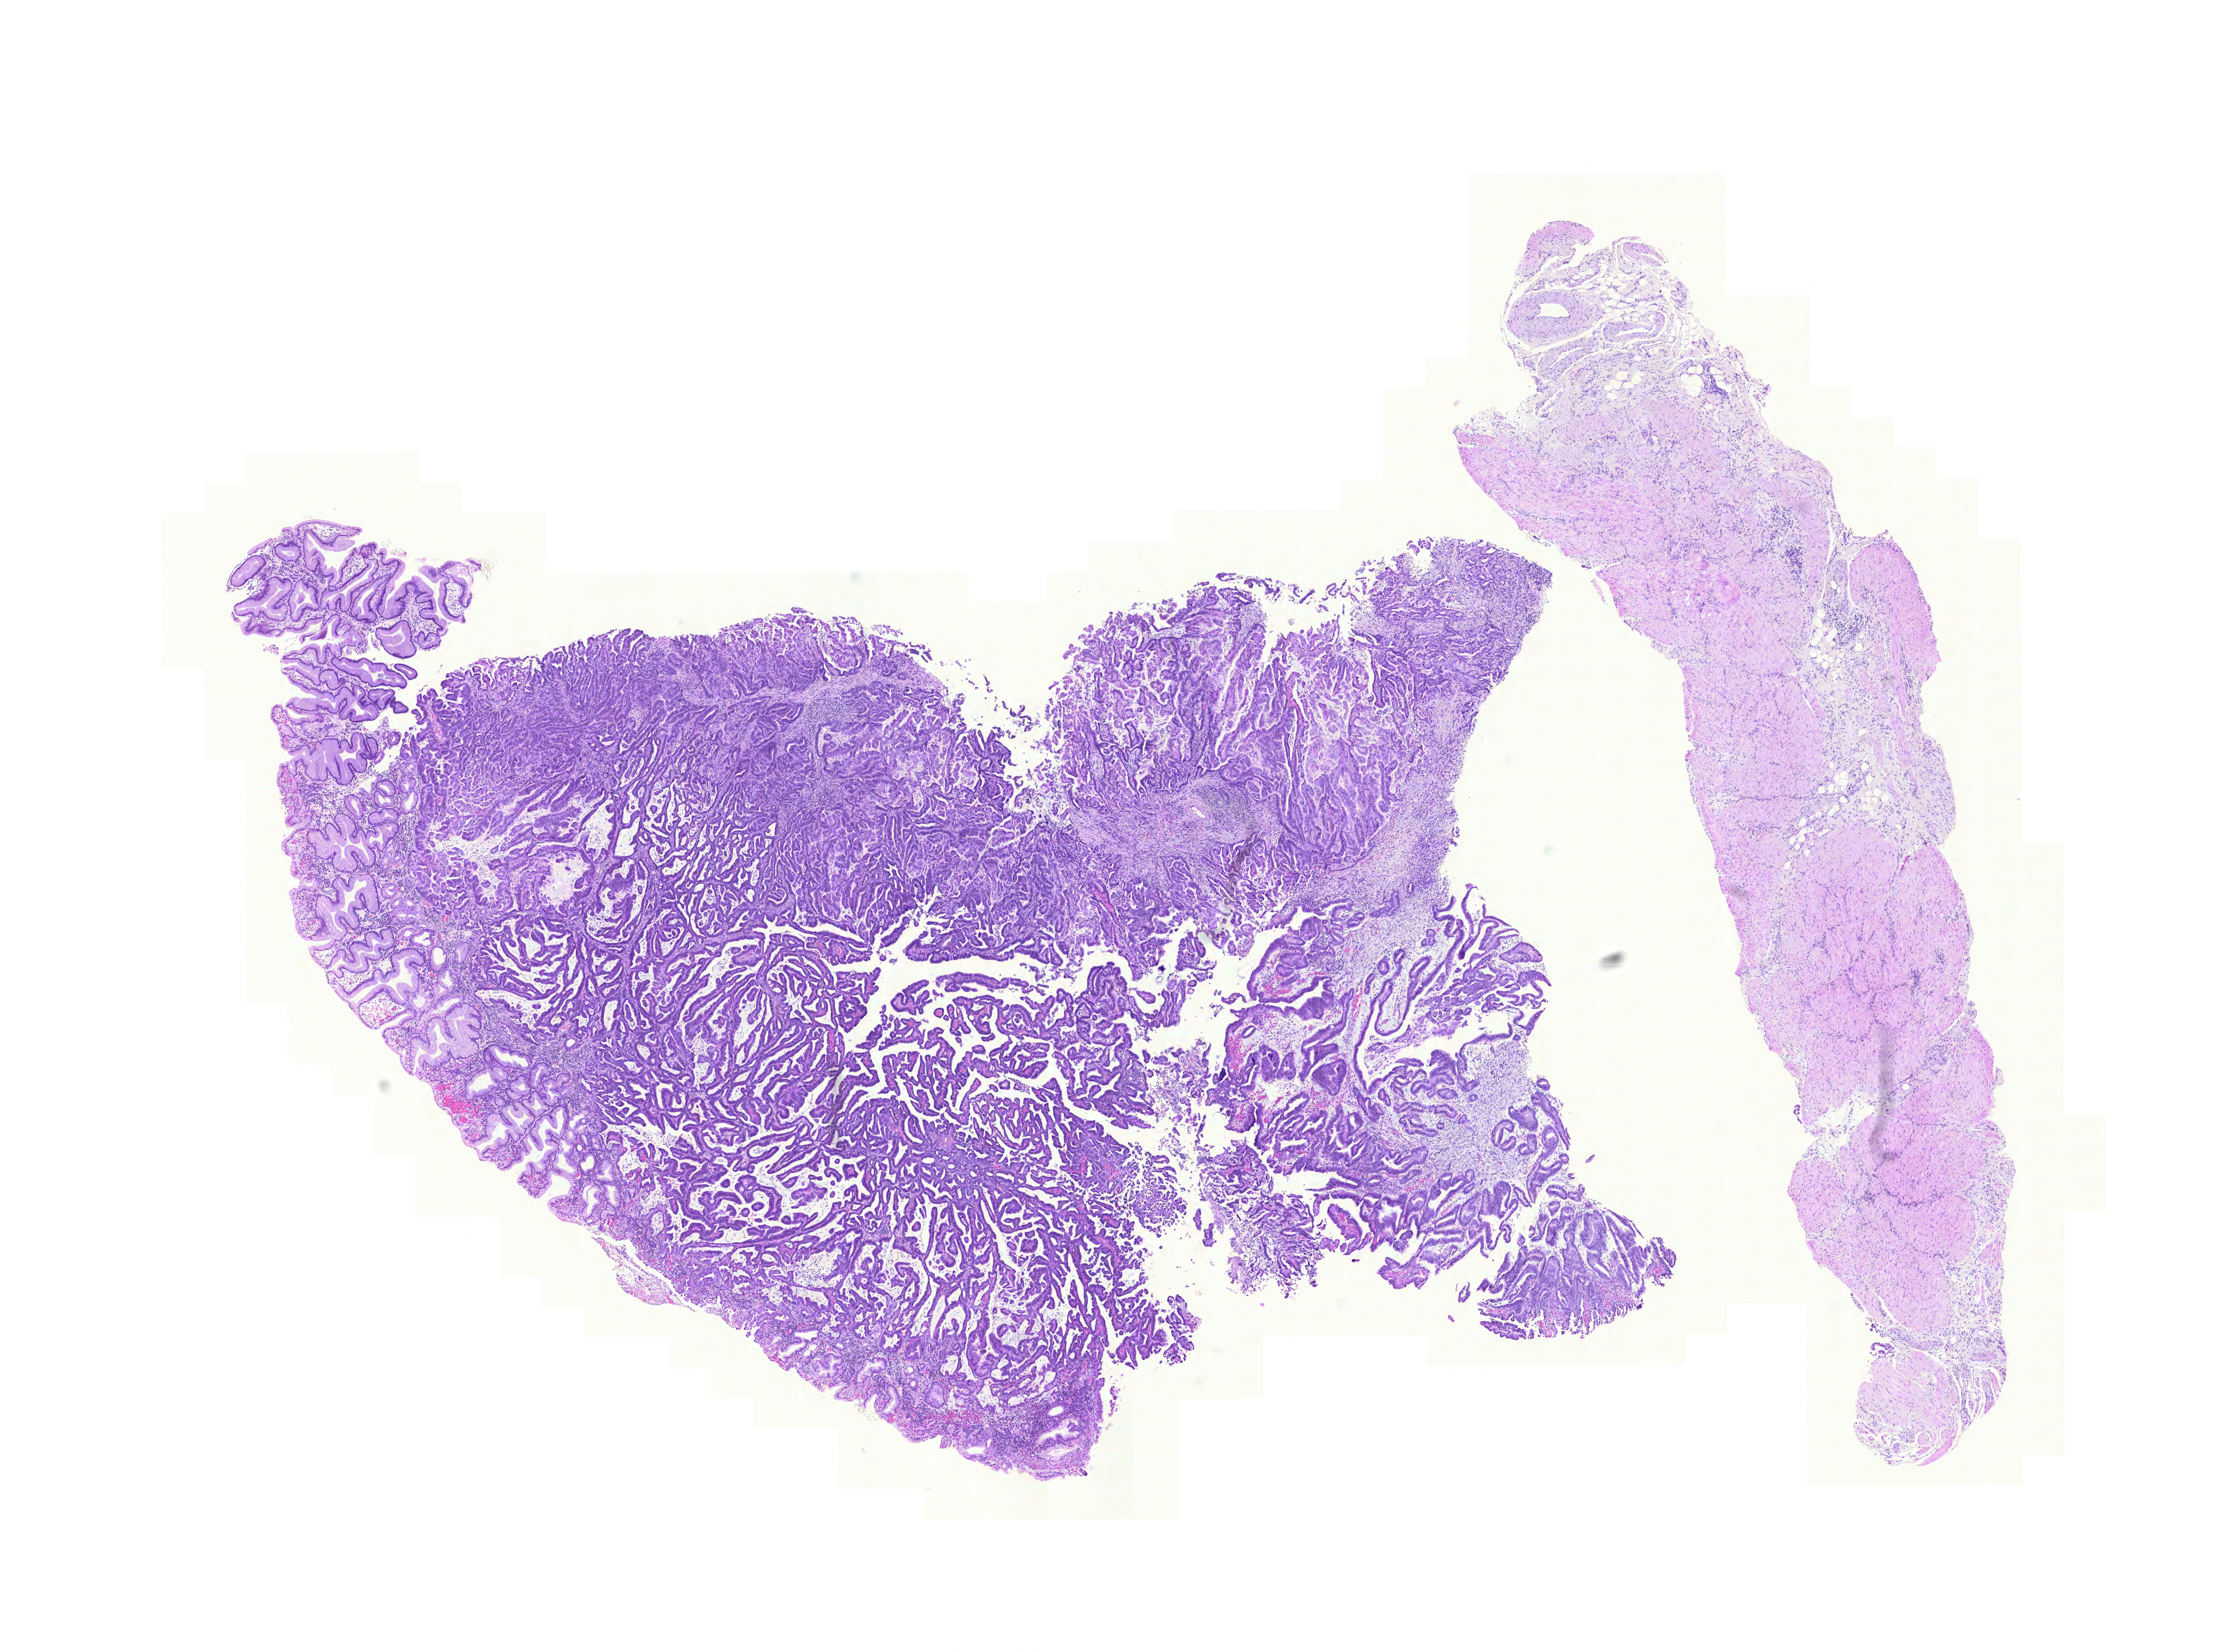
Hematoxylin and eosin (H&E) stained whole-slide image, whole scanned area (about 15.2 x 11.2 mm, slide scanned at 20x) shown as a low-resolution overview. Formalin-fixed paraffin-embedded (FFPE) diagnostic section. Stomach, primary tumour sample. Patient: male, age at initial diagnosis 69 years. Histologic grade: G3 (poorly differentiated).
Diagnosis: Adenocarcinoma, NOS (gastric antrum). AJCC pathologic stage: II. Lymph nodes positive (case pathology): 2 of 41 examined.